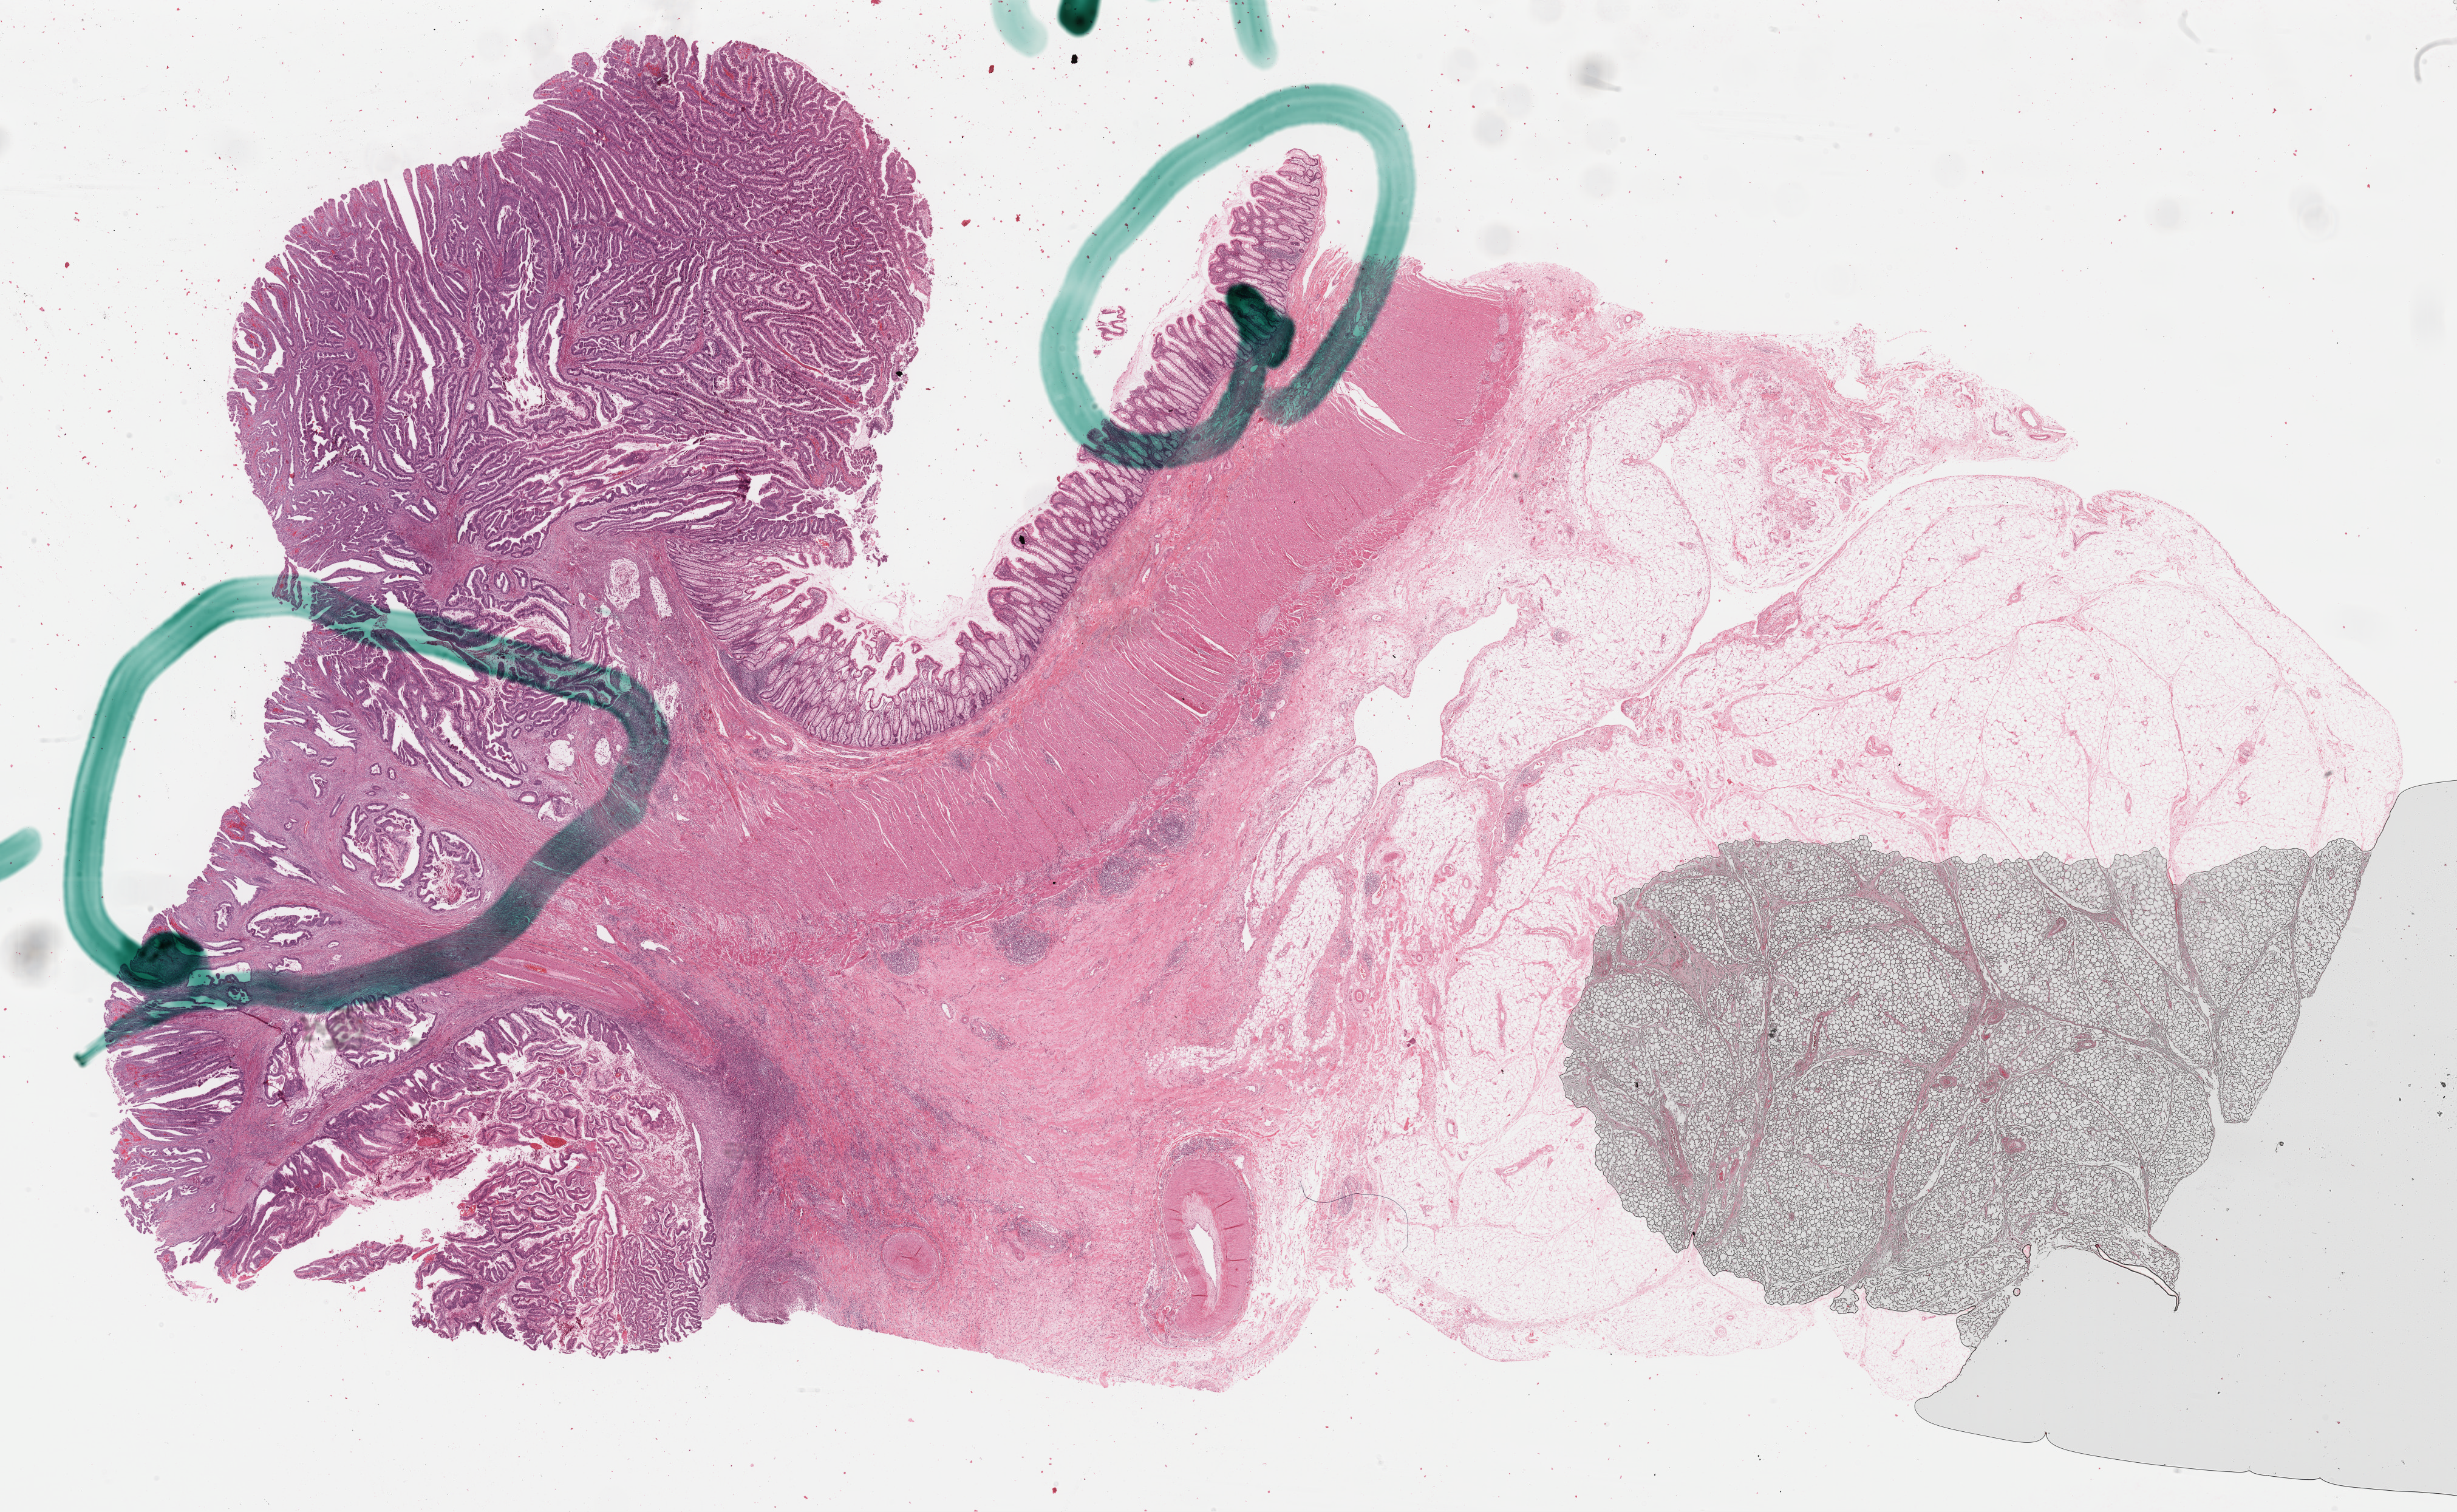
H&E-stained whole-slide image — a low-resolution overview of the entire scanned area, about 32.0 x 19.7 mm. Formalin-fixed paraffin-embedded (FFPE) diagnostic section. Colon, primary tumour sample. Female, age 60 years at initial diagnosis.
AJCC pathologic stage: IIA. Lymph nodes positive (case pathology): 0 of 16 examined. Diagnosis: Mucinous adenocarcinoma (hepatic flexure of colon).